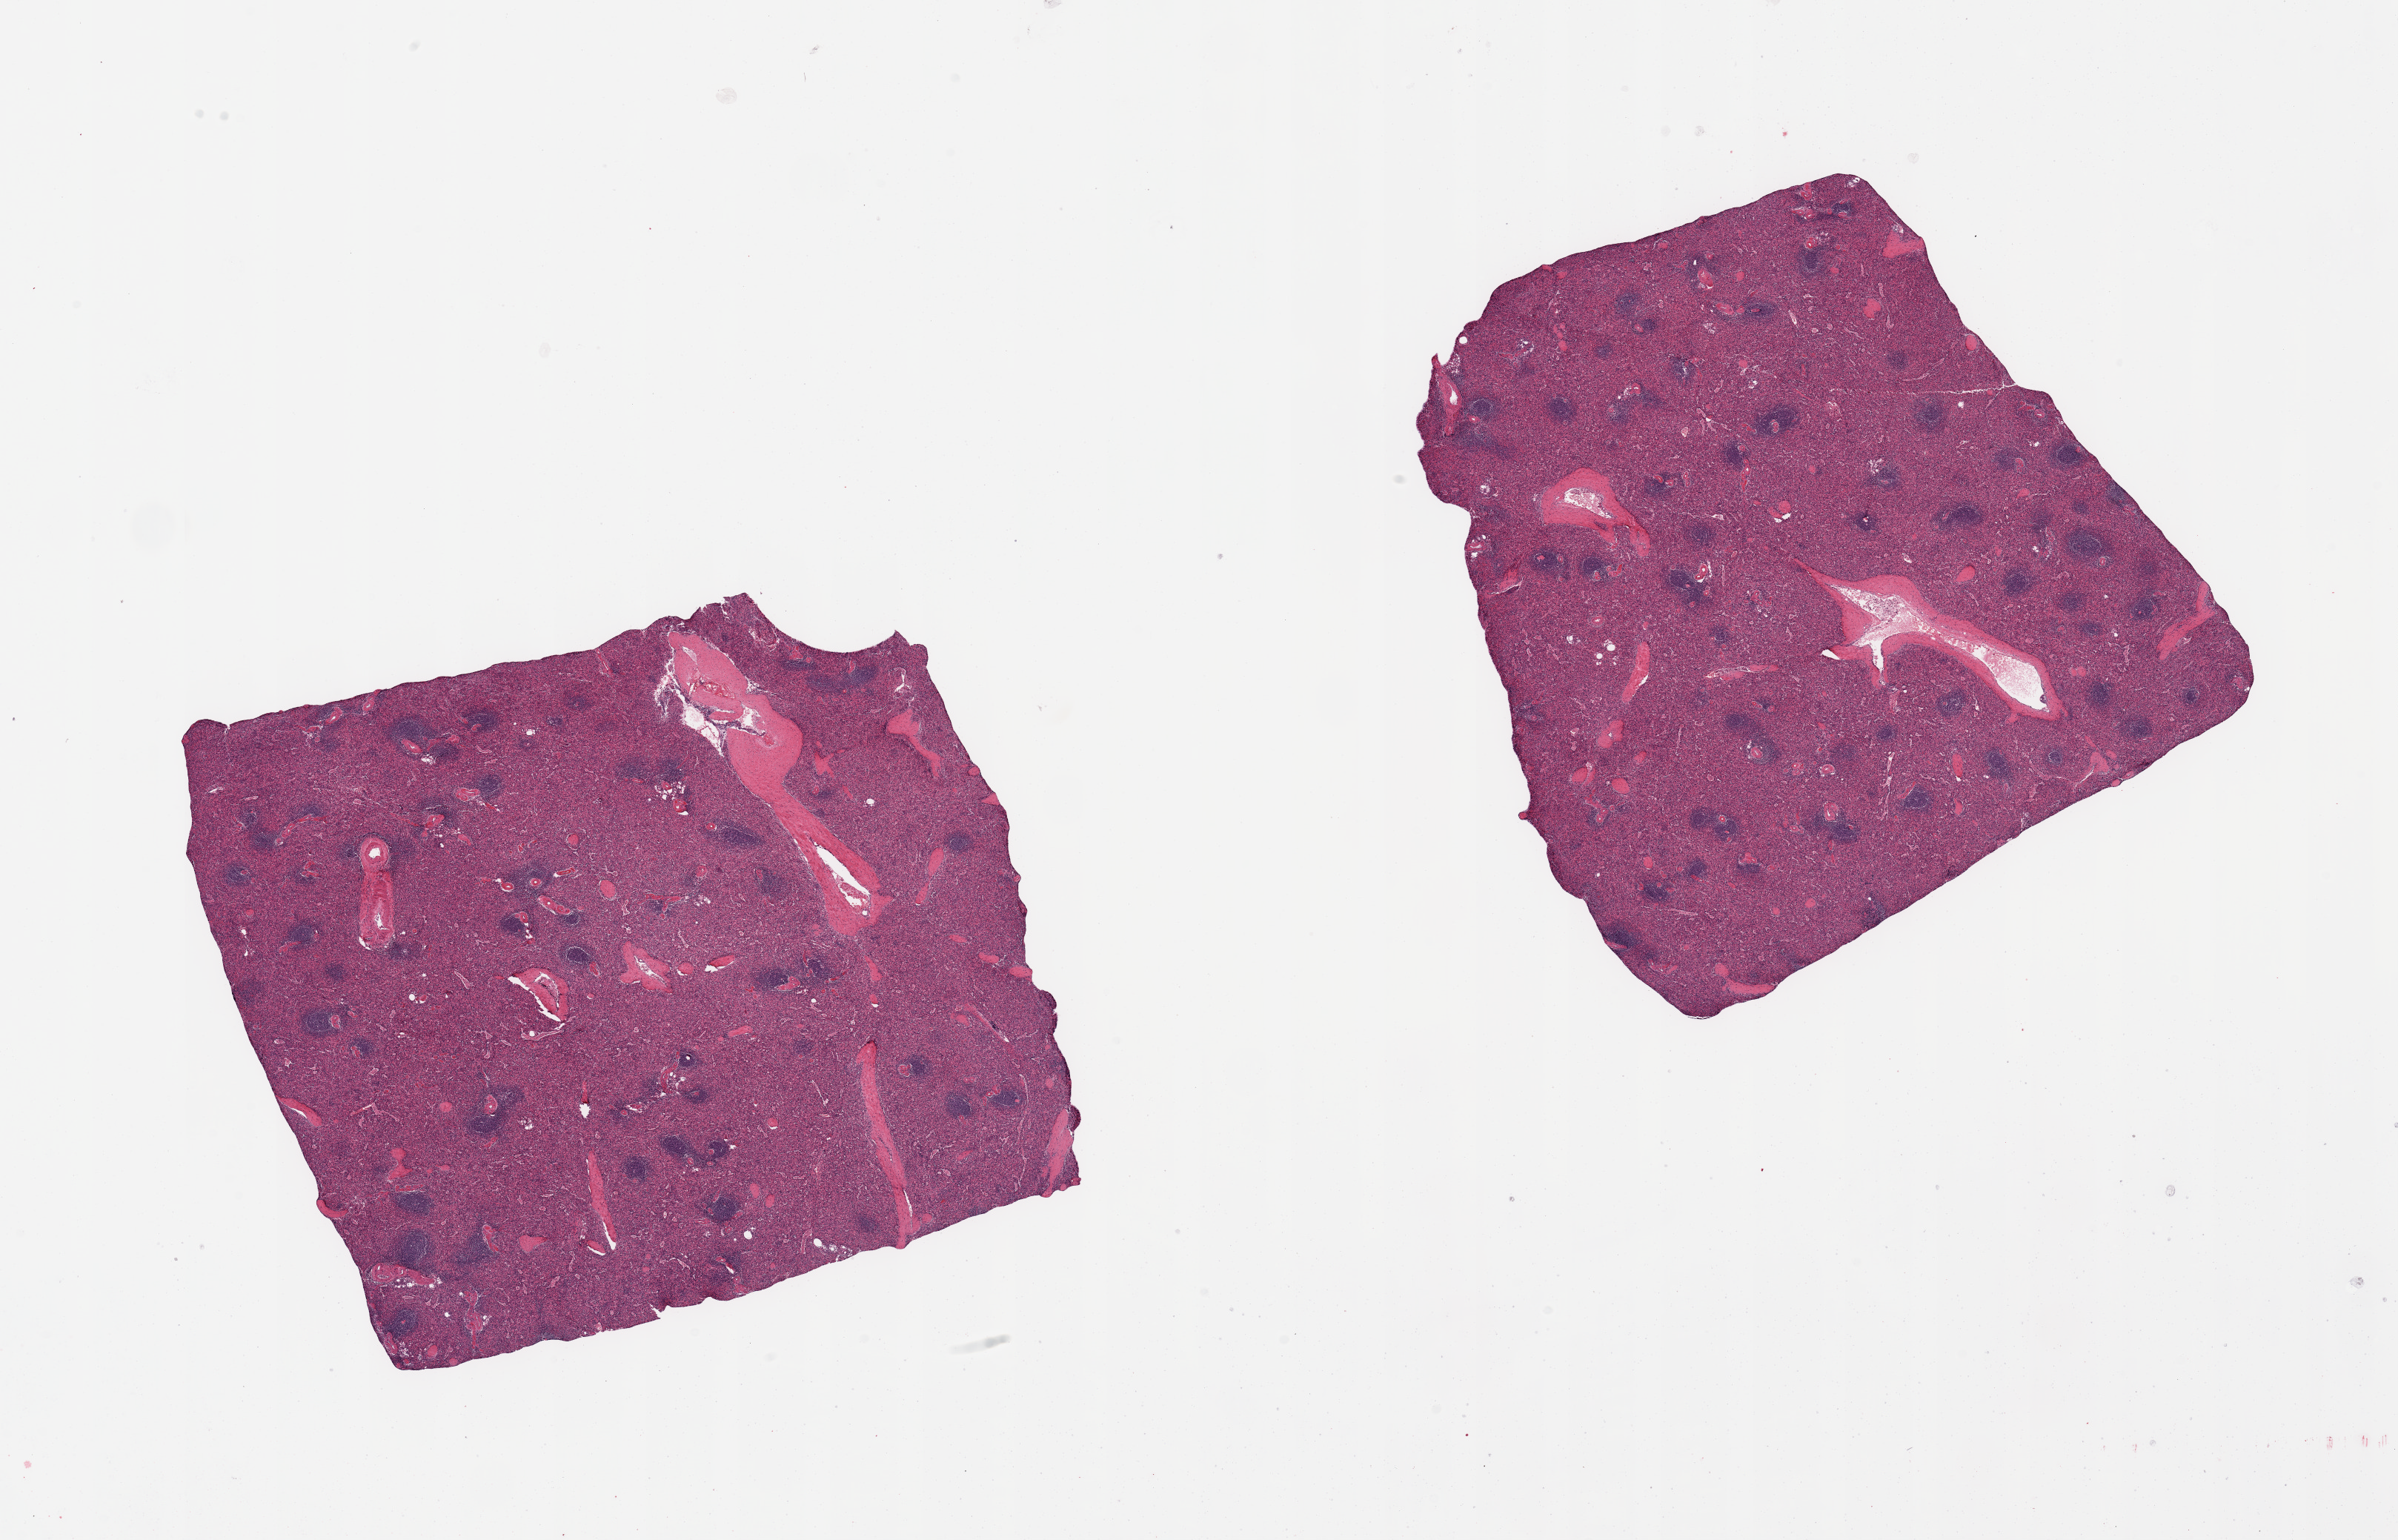
Hematoxylin and eosin (H&E) whole-slide image — a low-resolution overview of the entire scanned area, about 25.6 x 16.4 mm; PAXgene-fixed paraffin-embedded (PFPE) section; target tissue: spleen; donor tissue sample.
• pathologist's review note for this sample: 2 pieces; slight congestion